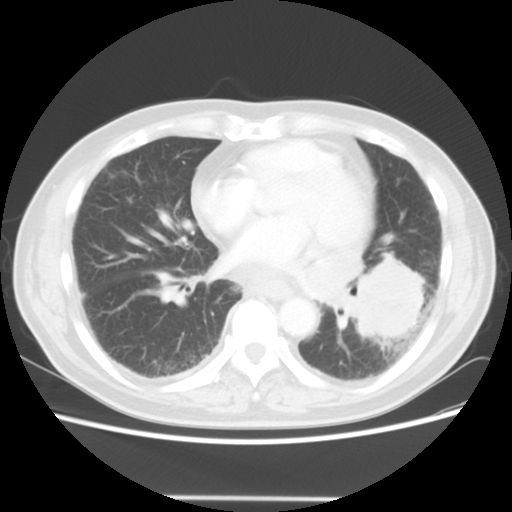
Chest CT, one axial slice. Reconstruction kernel STANDARD. 140 kVp. Lung window (W 1500 / L -600 HU). 512 × 512 image matrix. Male patient, age 66 years. Case-level facts recorded for this patient, not image findings: clinical TNM (as recorded): T4 N3 M0.
Annotated regions visible in this slice (rectangle marked by the reading radiologist):
- lung tumour (recorded histology: small cell carcinoma): bounding box [x1, y1, x2, y2] px = [354, 248, 434, 358]